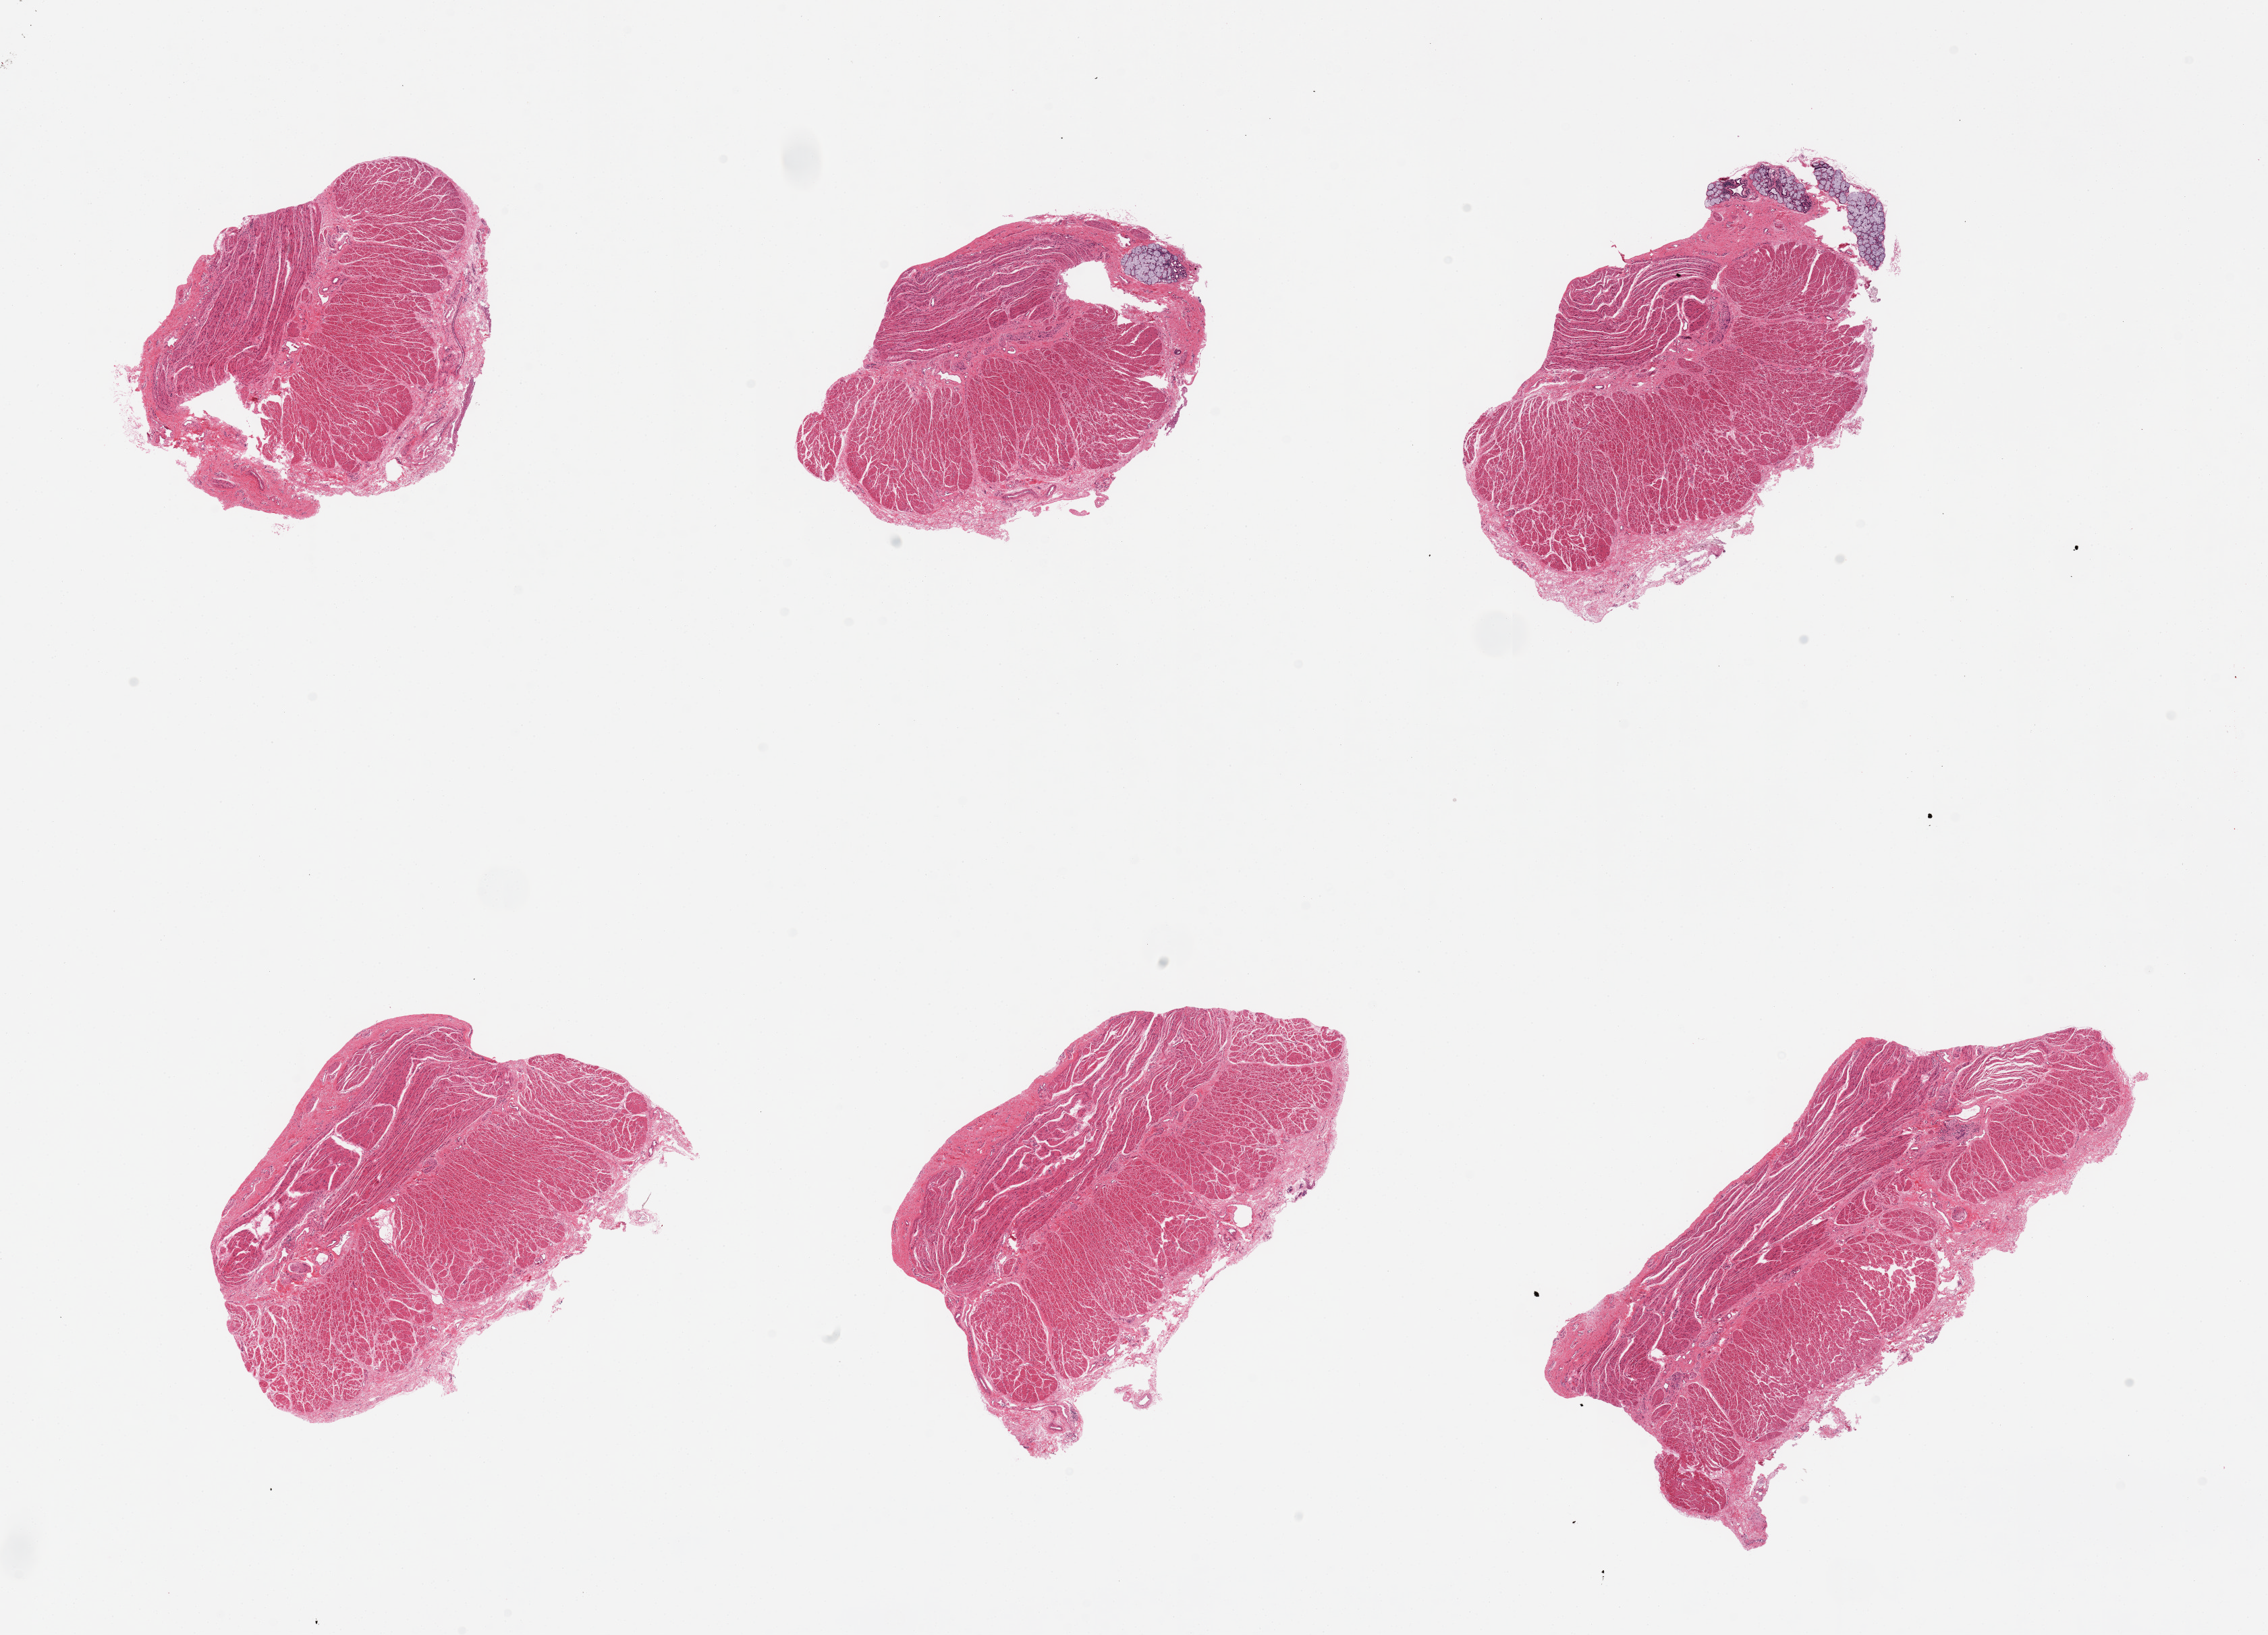
Digitized hematoxylin and eosin (H&E)-stained section, low-resolution overview of the scanned area, about 26.6 x 19.2 mm (slide scanned at 20x); PAXgene-fixed, paraffin-embedded tissue; target tissue: gastroesophageal junction; donor tissue sample.
• review note (as recorded): 6 pieces; 2 with submucosal glands on edge up to 2 x 0.5mm